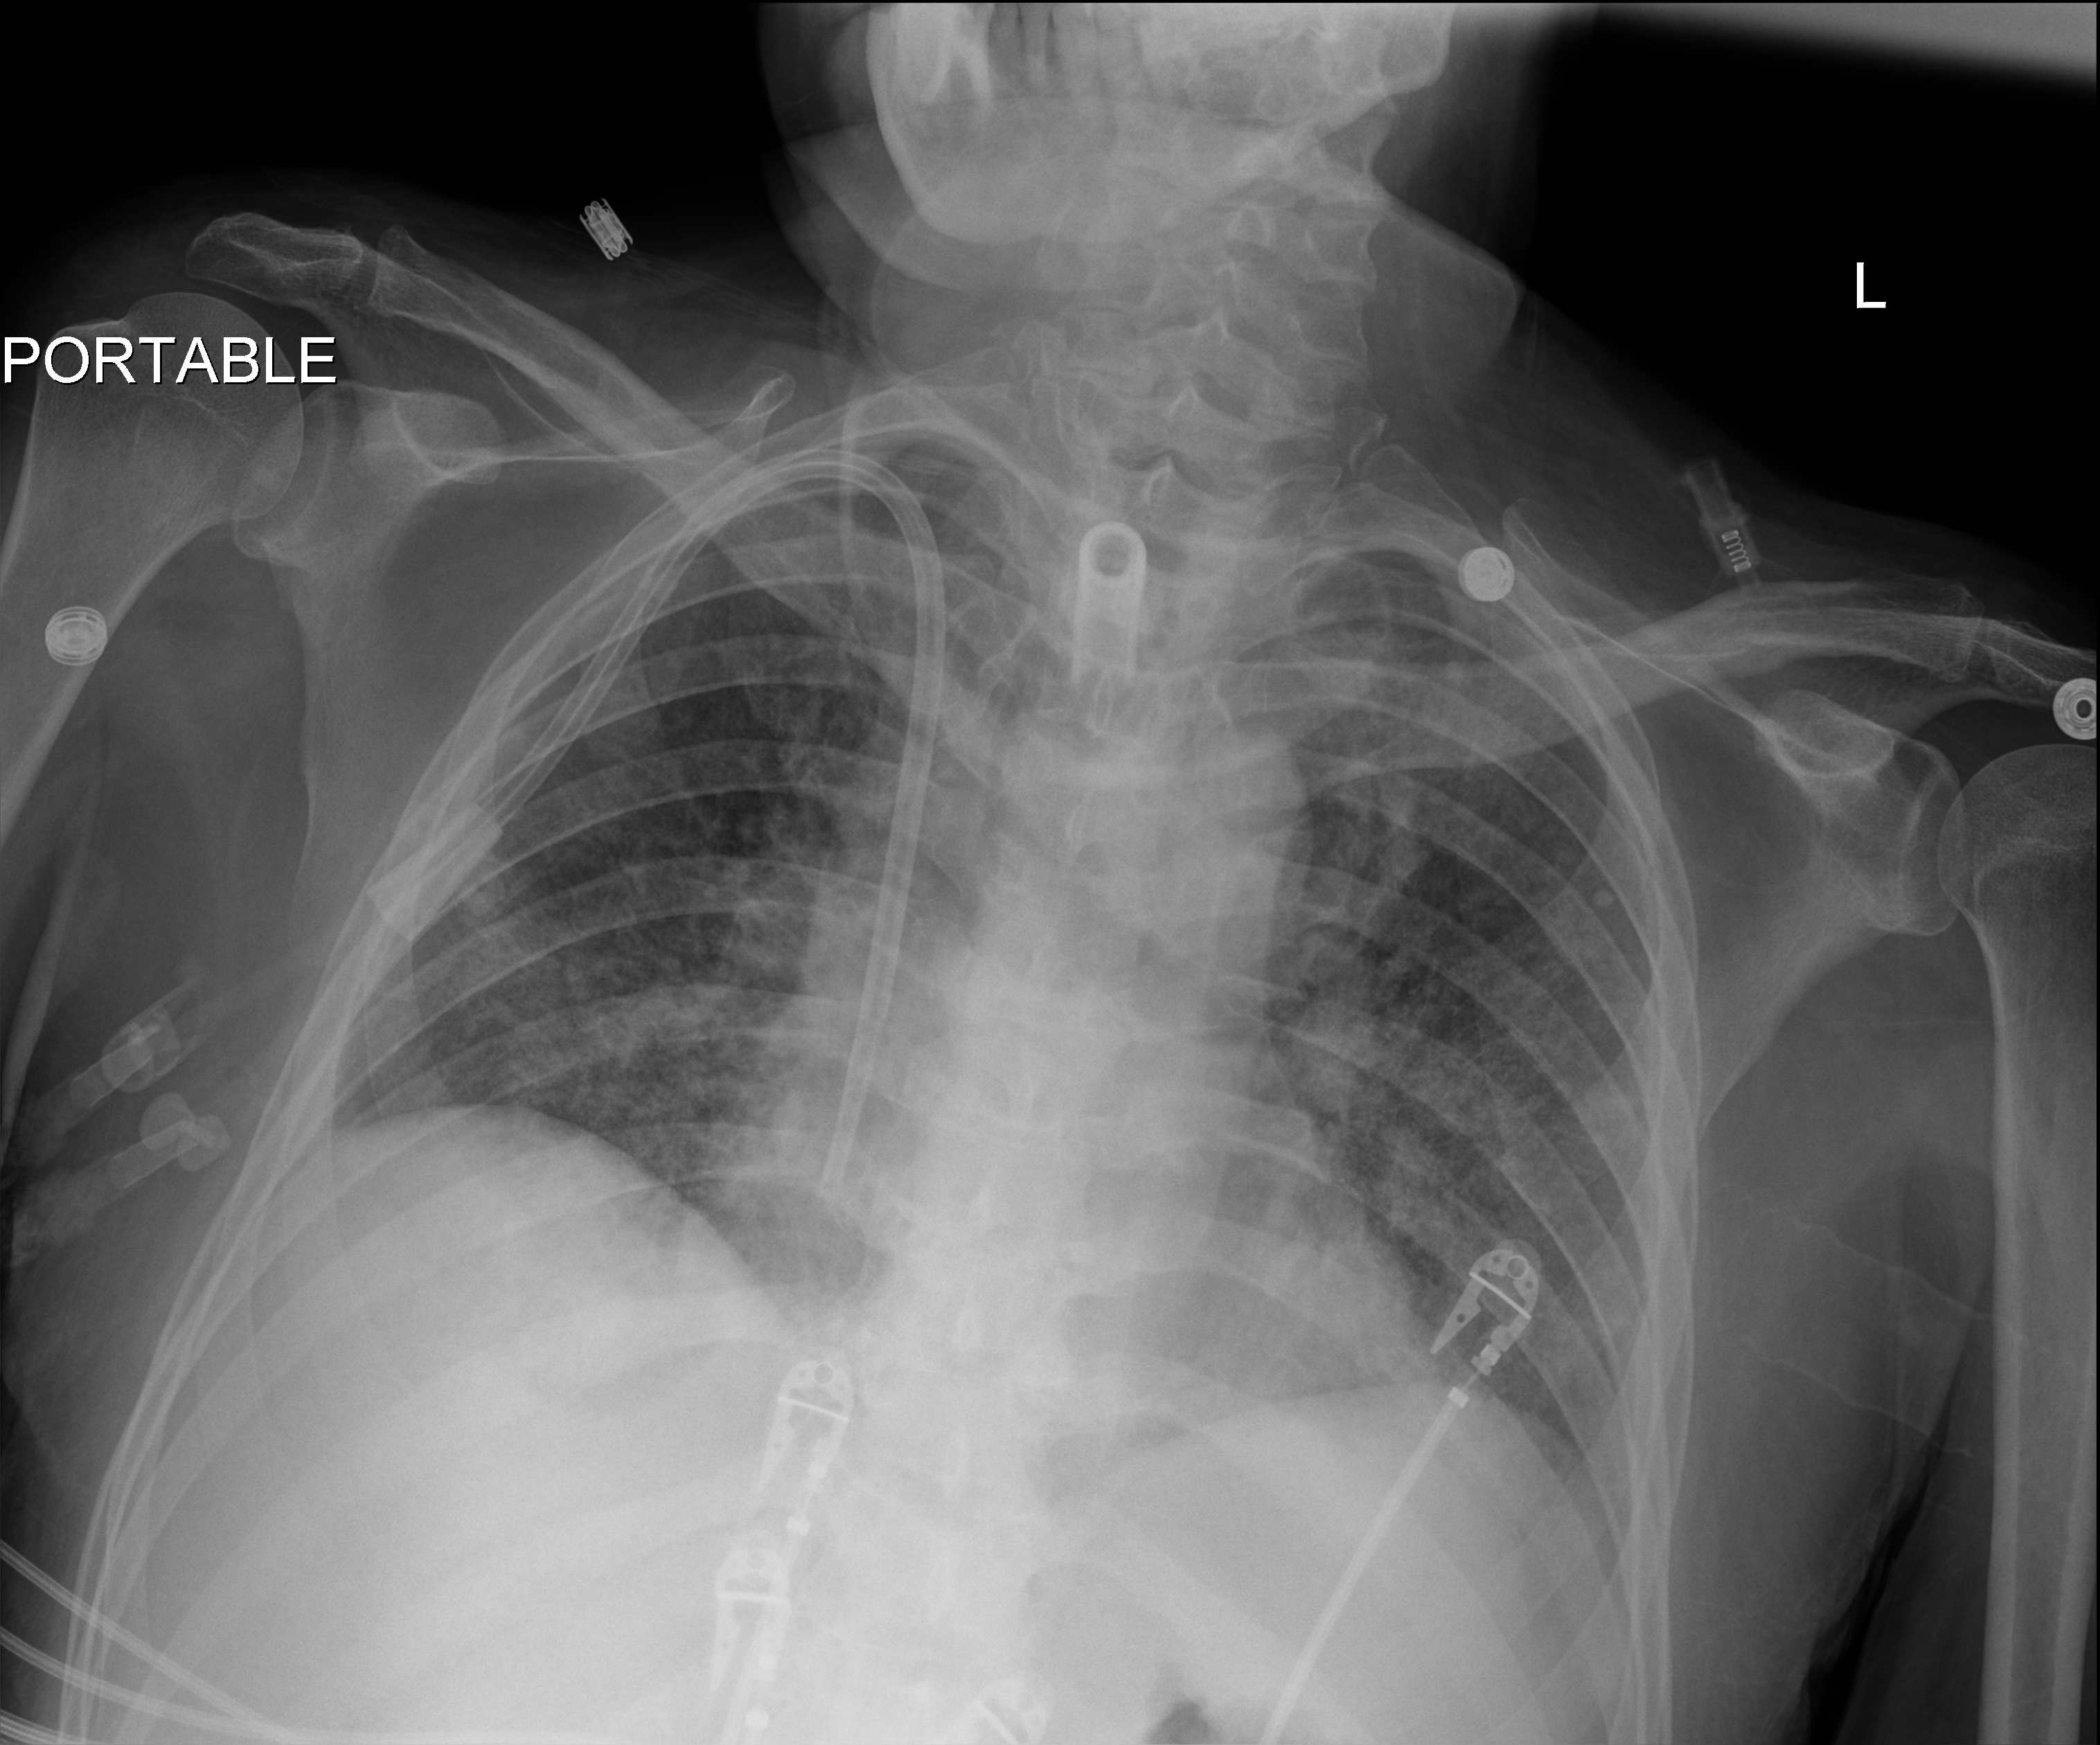
Portable chest radiograph, anteroposterior (AP) projection. Male patient hospitalised with COVID-19, age 18–59 years.
From the hospital-stay record, not from the radiograph (when in the stay this image was taken is not recorded): length of hospital stay: 77 days; COPD (admission record): no.